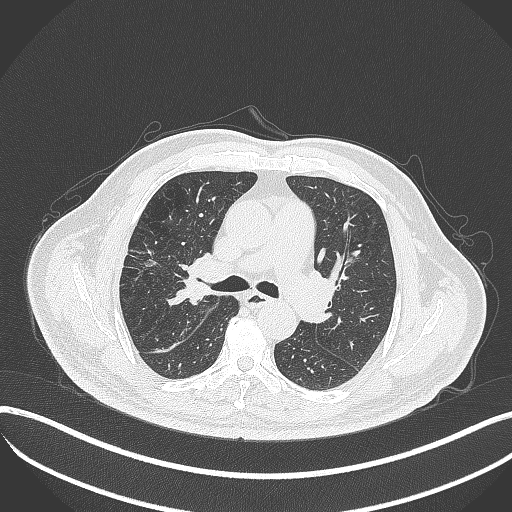
Chest CT, one axial slice; position 226 of 401 along the scan axis; reconstruction kernel B70f; lung window (W 1500 / L -600 HU); 1 mm slice thickness; 512 × 512 image matrix, field of view 400 × 400 mm. Male patient, age 72 years. Case-level facts recorded for this patient, not image findings: clinical TNM (as recorded): T1c N0 M0.
Annotated regions visible in this slice (bounding box drawn by a radiologist):
- lung tumour (recorded histology: squamous cell carcinoma): box from (x=161, y=257) to (x=209, y=316) px